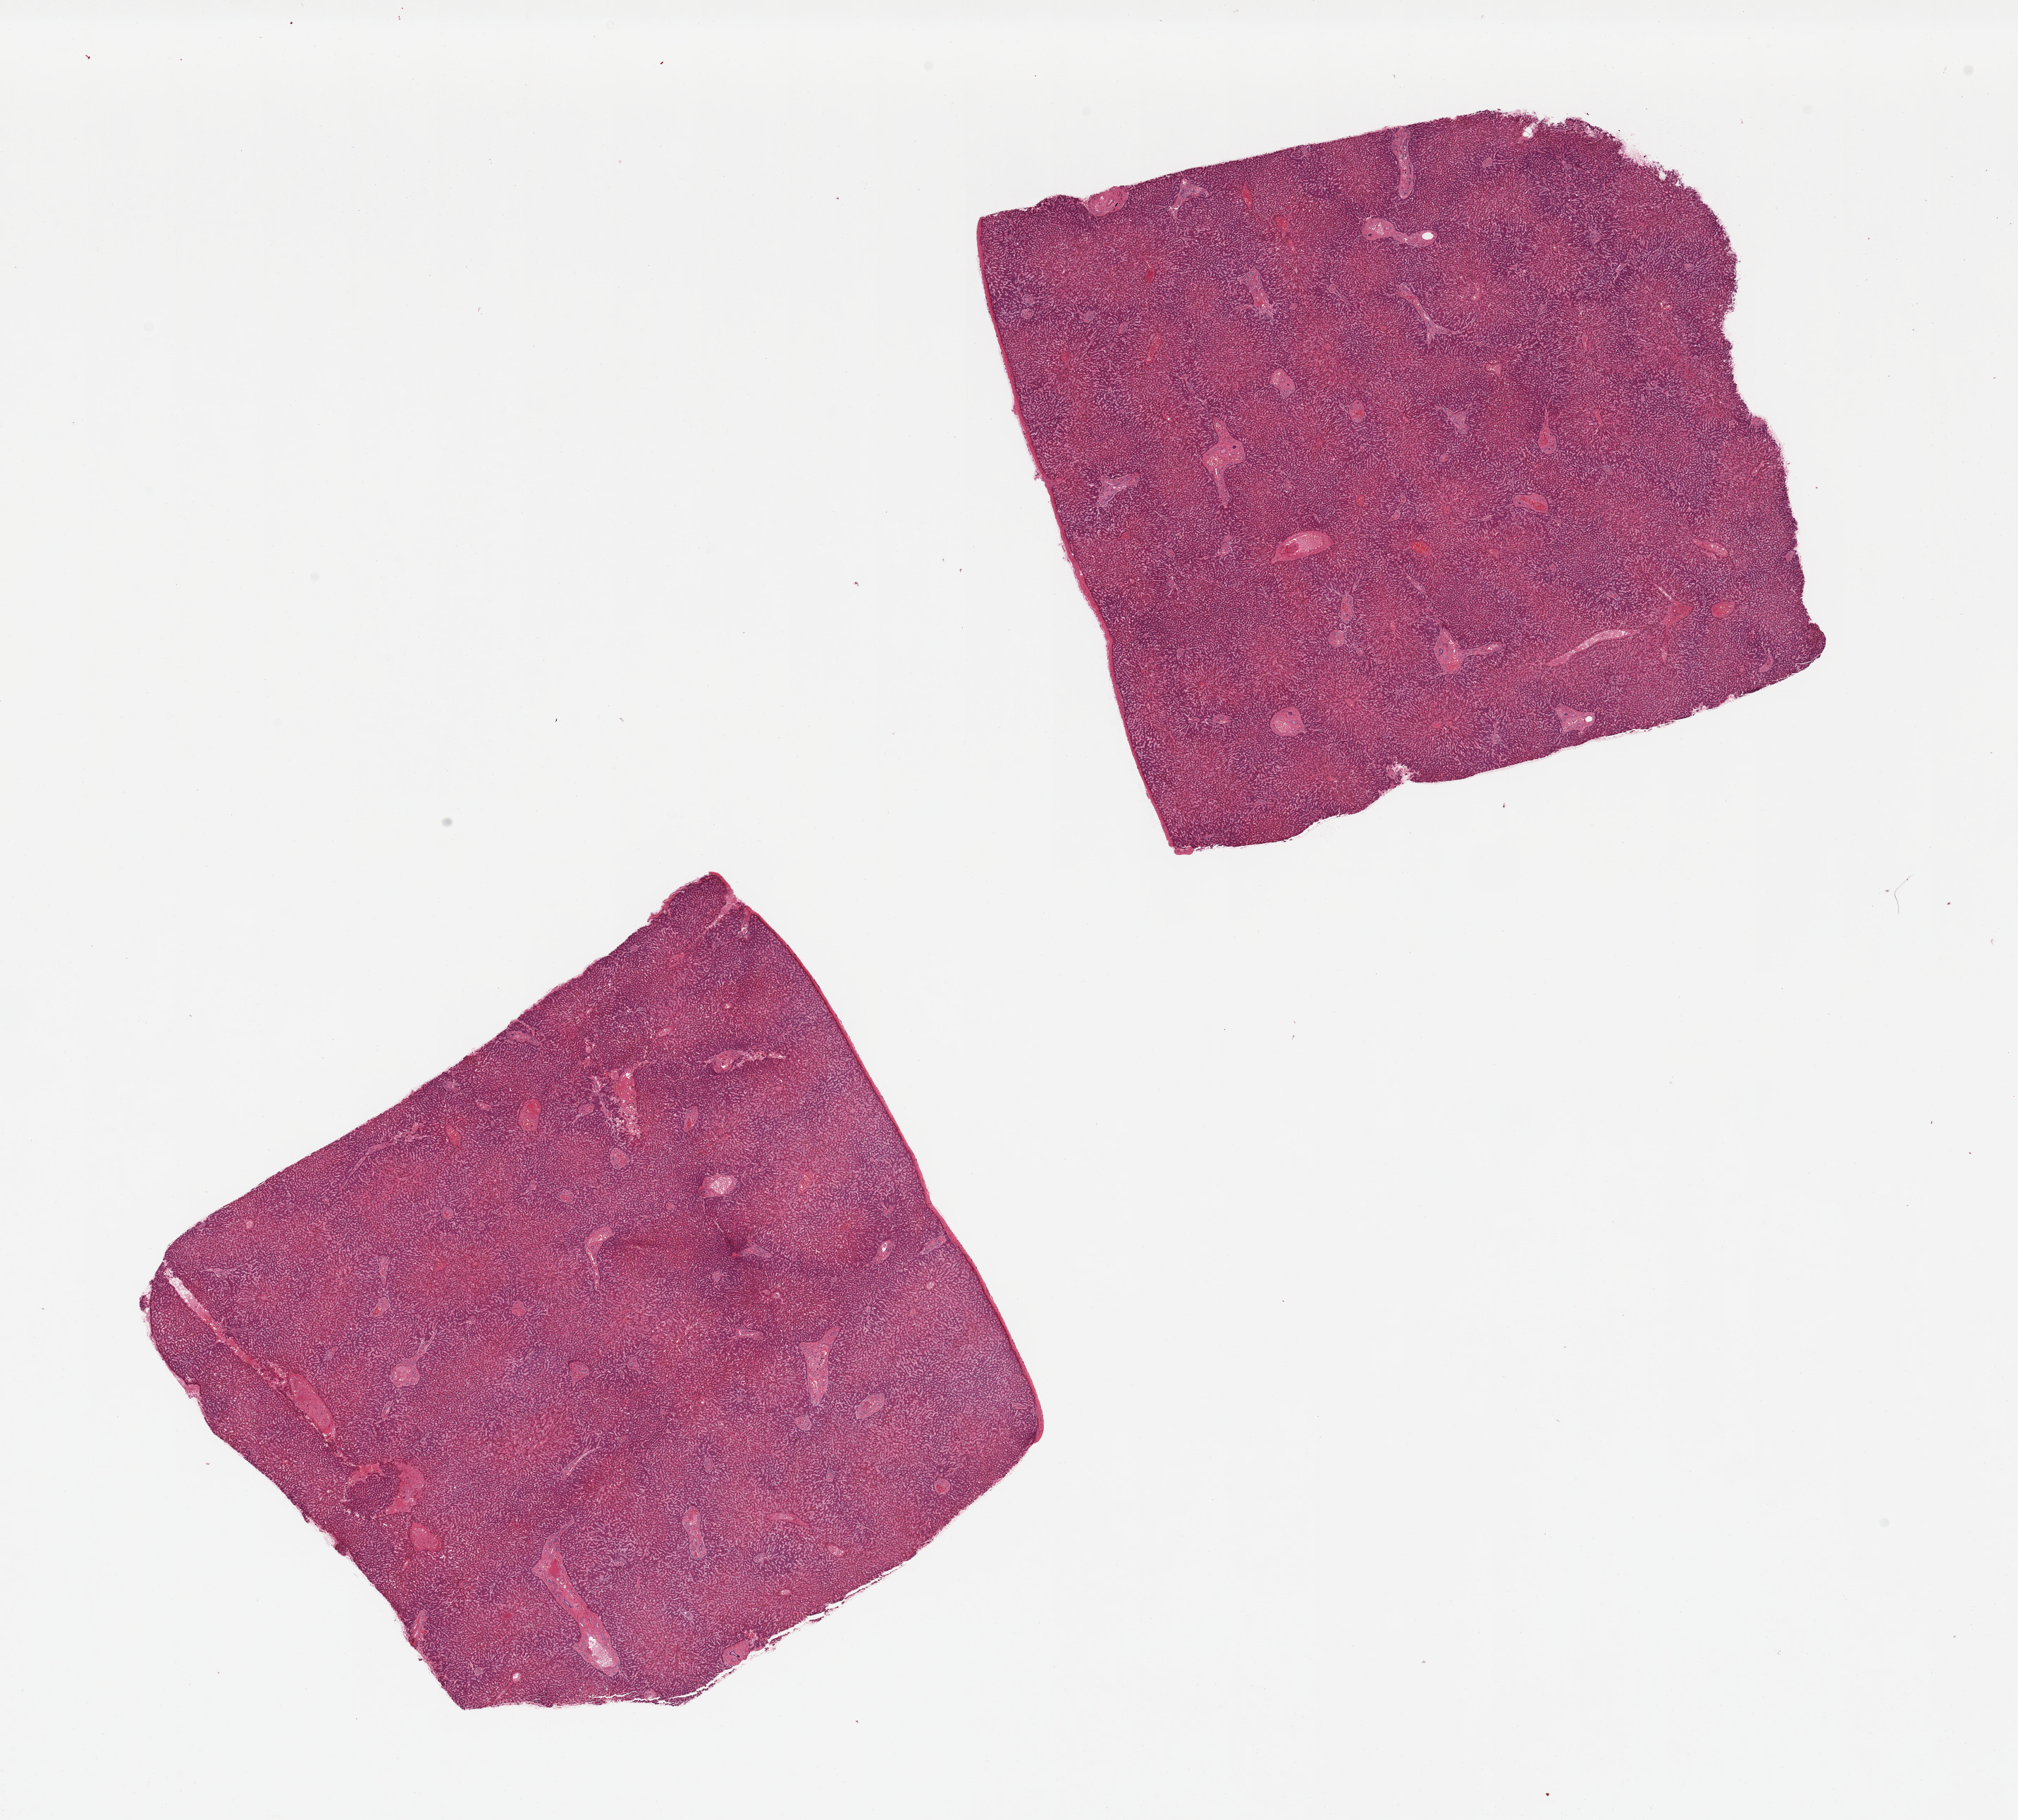
H&E whole-slide image — a low-resolution overview of the entire scanned area, about 22.6 x 20.4 mm (slide scanned at 20x), PAXgene-fixed, paraffin-embedded tissue, target tissue: liver, tissue donor sample. Female donor.
Pathologist's review note for this sample: 2 pieces, centrilobular congestion.